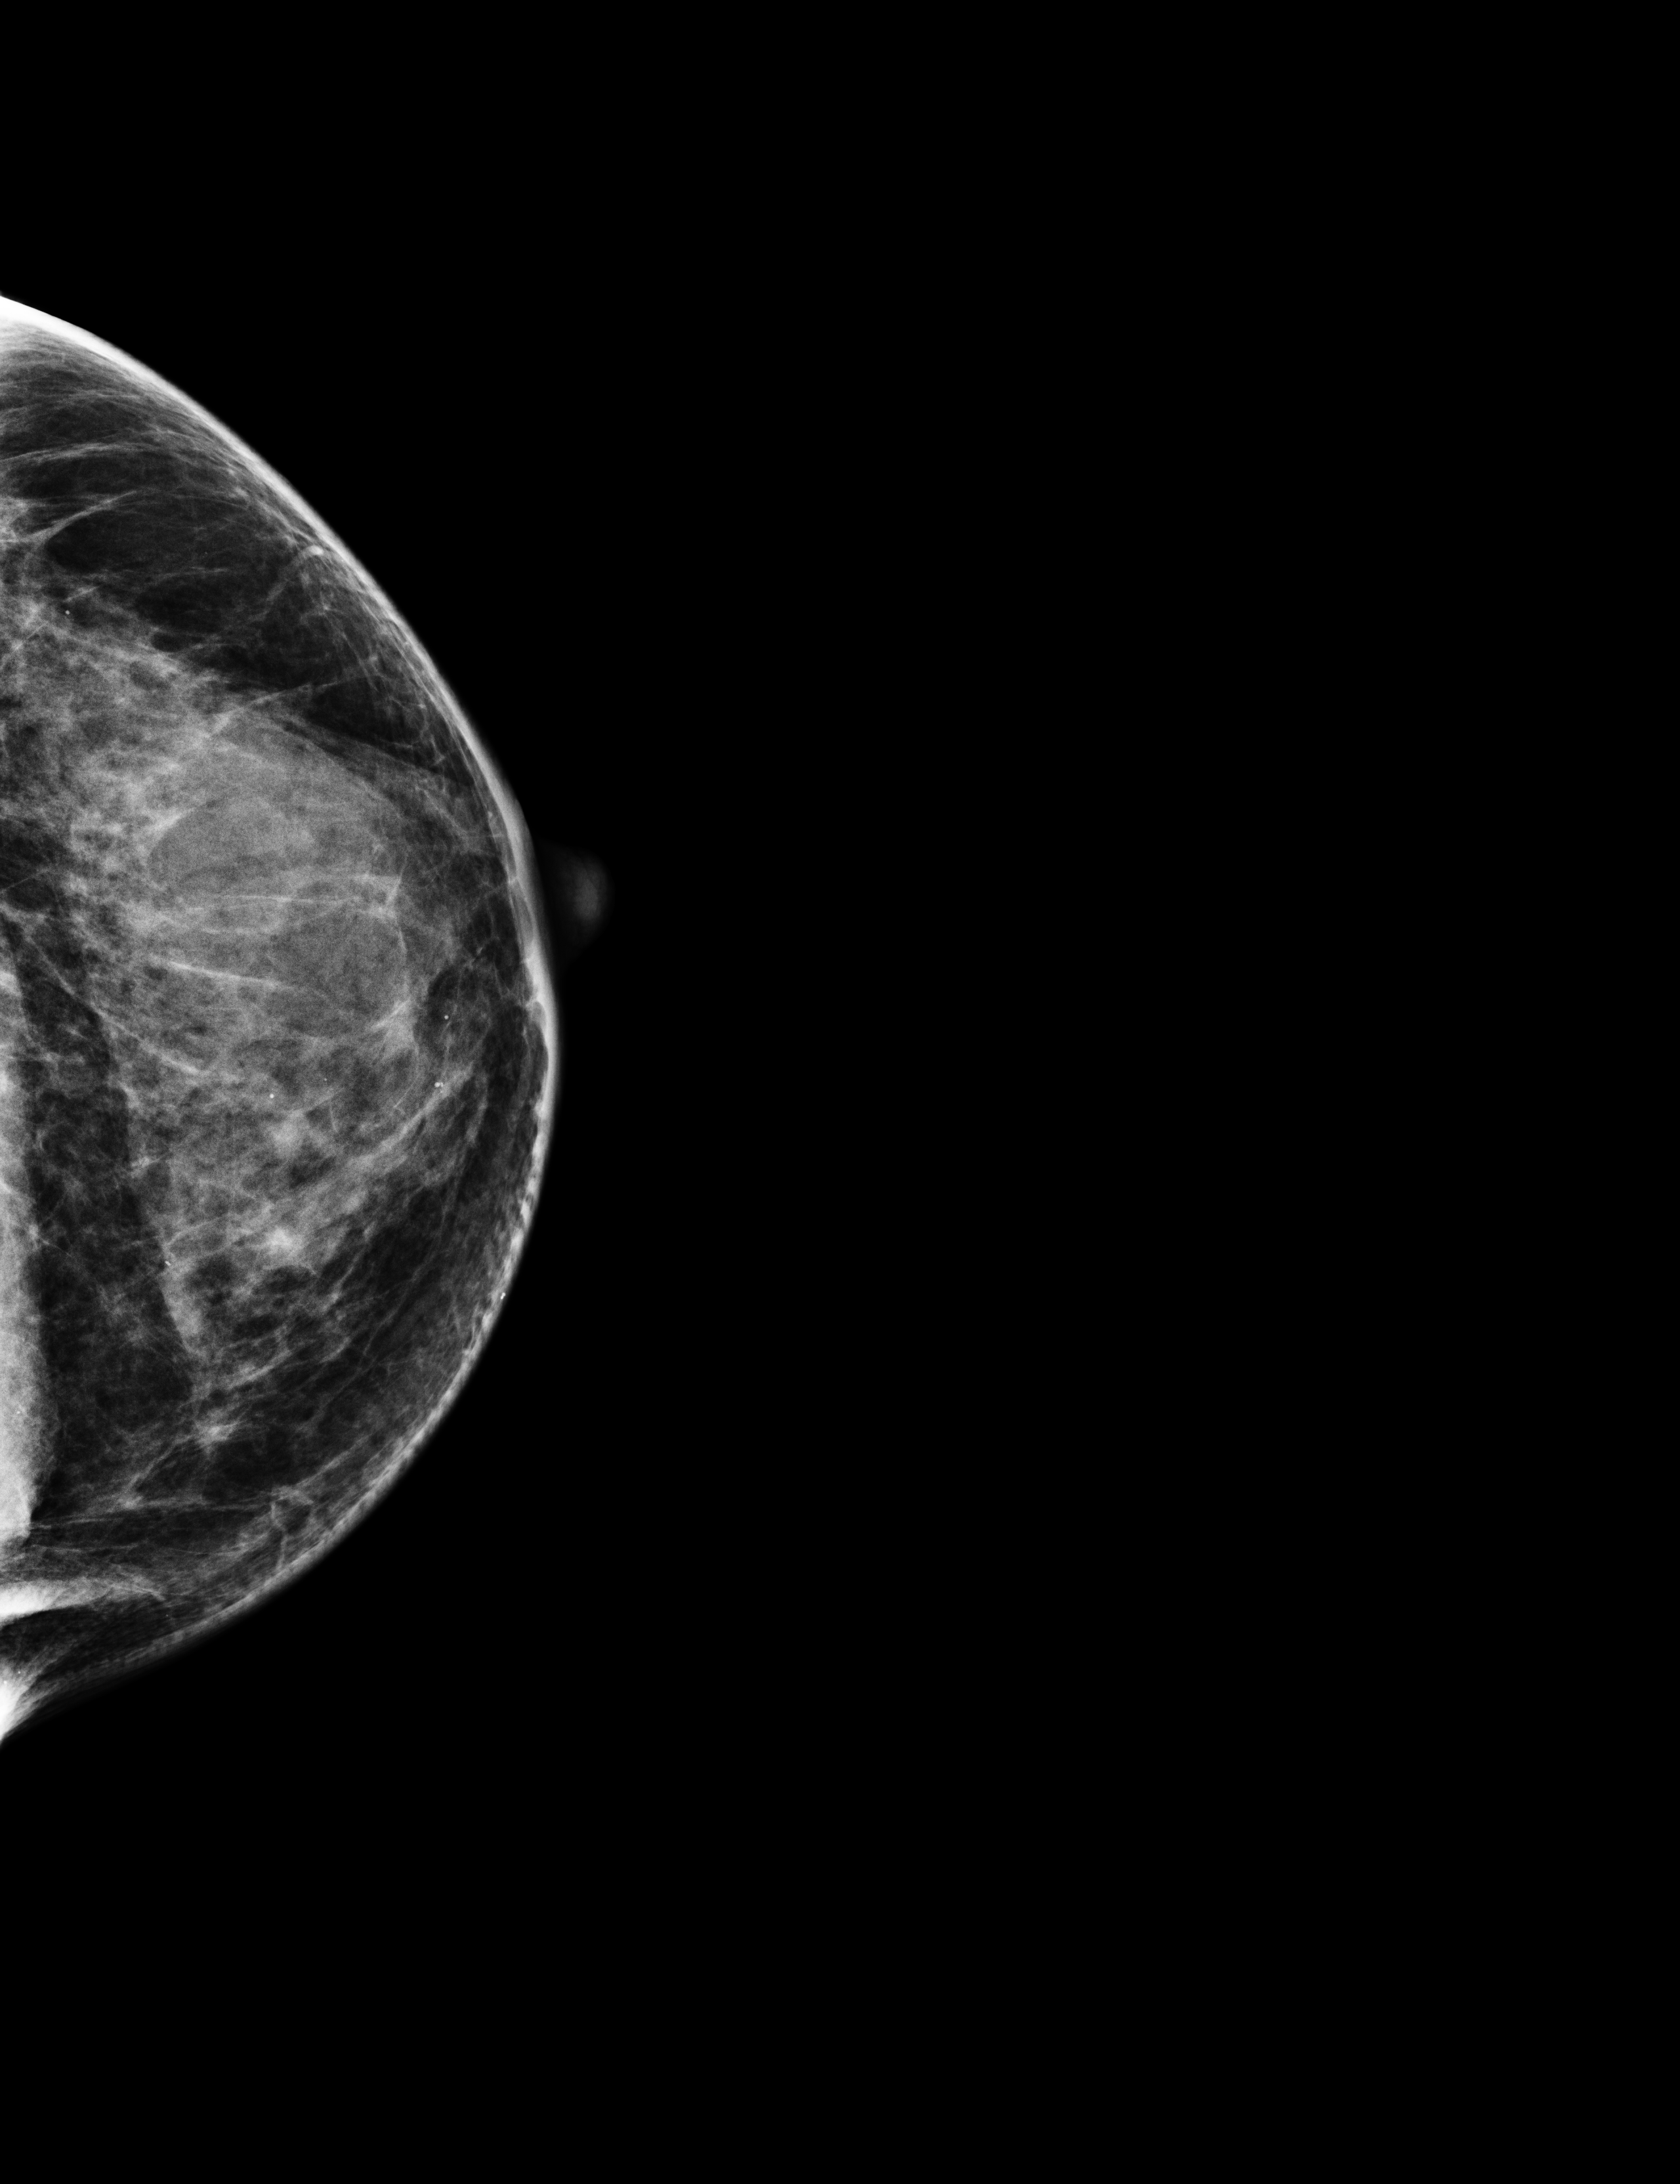
Annual screening mammography examination, compressed breast thickness 59 mm. Female patient, age 56 years.
Image type: full-field digital mammogram. Breast: left. Projection: craniocaudal (CC) view.